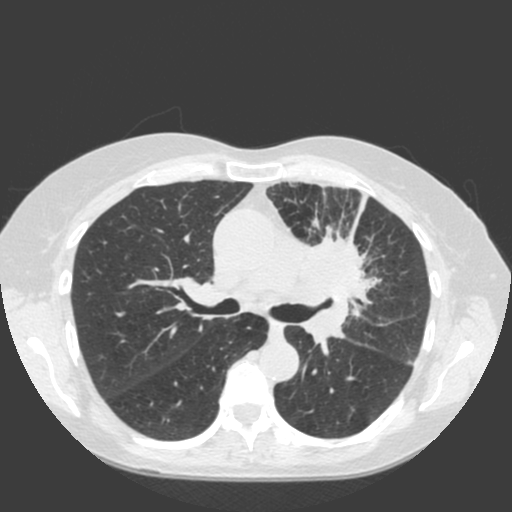
Axial slice from a low-dose chest CT screening exam; baseline screening round; lung window (W 1500 / L -600 HU); 2 mm slice thickness; standard (soft-tissue) reconstruction kernel (C); slice 67 of 184 in the series. Female participant, aged 66 years at enrolment. Current smoker at enrolment.
• Expert reader's lesion annotation, box from (x=279, y=212) to (x=401, y=322) px.
• The exam's reader record, not a measurement of the box and not confirmed to be the same lesion: non-calcified nodule or mass ≥4 mm, left upper lobe, 61 × 45 mm, spiculated (stellate) margins, soft tissue attenuation.
• Official screen result: positive, change unspecified: nodule(s) >= 4 mm or enlarging nodule(s), mass(es), or other non-specific abnormalities suspicious for lung cancer.